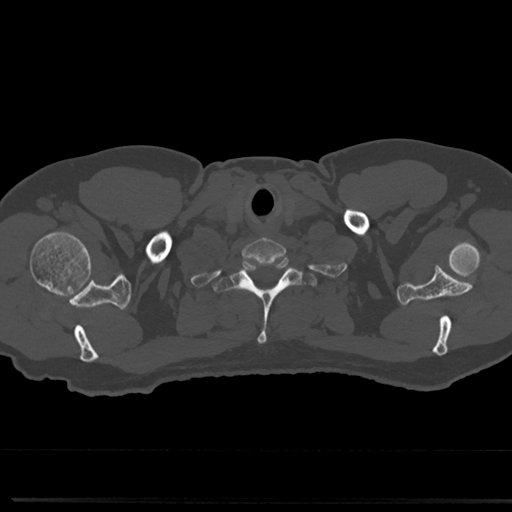
CT including the spine, one axial slice; reconstruction kernel Br40s/3; 120 kVp; bone window (W 1800 / L 400 HU); 512 × 512 image matrix, field of view 355 × 355 mm. Male patient, age 61 years. Case-level facts recorded for this patient, not image findings: primary cancer: prostate.
Structures marked on this image (semi-automatically segmented with operator editing):
- T1 vertebra: box from (x=219, y=255) to (x=312, y=345) px